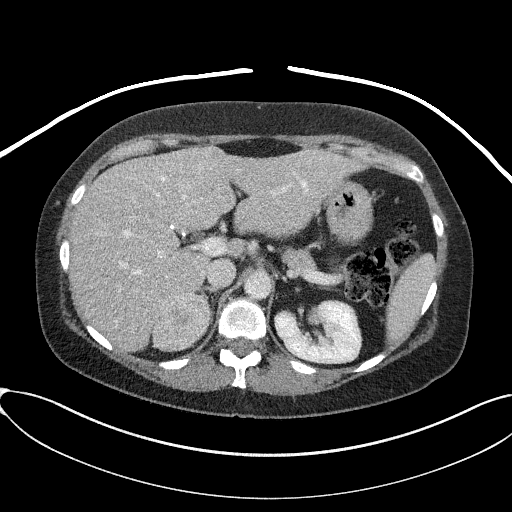
Contrast-enhanced abdominal CT, one axial slice. Slice 56 of 95 in the series (ordered by position). 100 kVp. Intravenous contrast given. Soft-tissue window (W 400 / L 40 HU). 3 mm slice thickness. 512 × 512 image matrix. Patient: female, 46 years. Case-level facts recorded for this patient, not image findings: diagnosis: adrenocortical carcinoma; tumour side: right adrenal; tumour size at pathology: 7.2 cm; Ki-67 index: 50 %.
Annotated regions visible in this slice (semi-automatically segmented with operator editing):
- mass: bounding box [x1, y1, x2, y2] px = [154, 292, 210, 349]